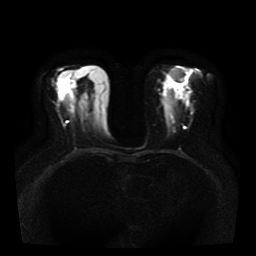
Breast MRI, one axial slice; position 20 of 41 along the scan axis; diffusion-weighted series; image 2 of 4 stored at this slice position (different b-values; order by instance number); 1.5 T; 5 mm slice thickness; 256 × 256 image matrix. Female patient.
Outlined on this slice (expert manual segmentation):
- tumour on diffusion-weighted imaging: bounding box <188,92,191,95> (left, top, right, bottom; pixels)